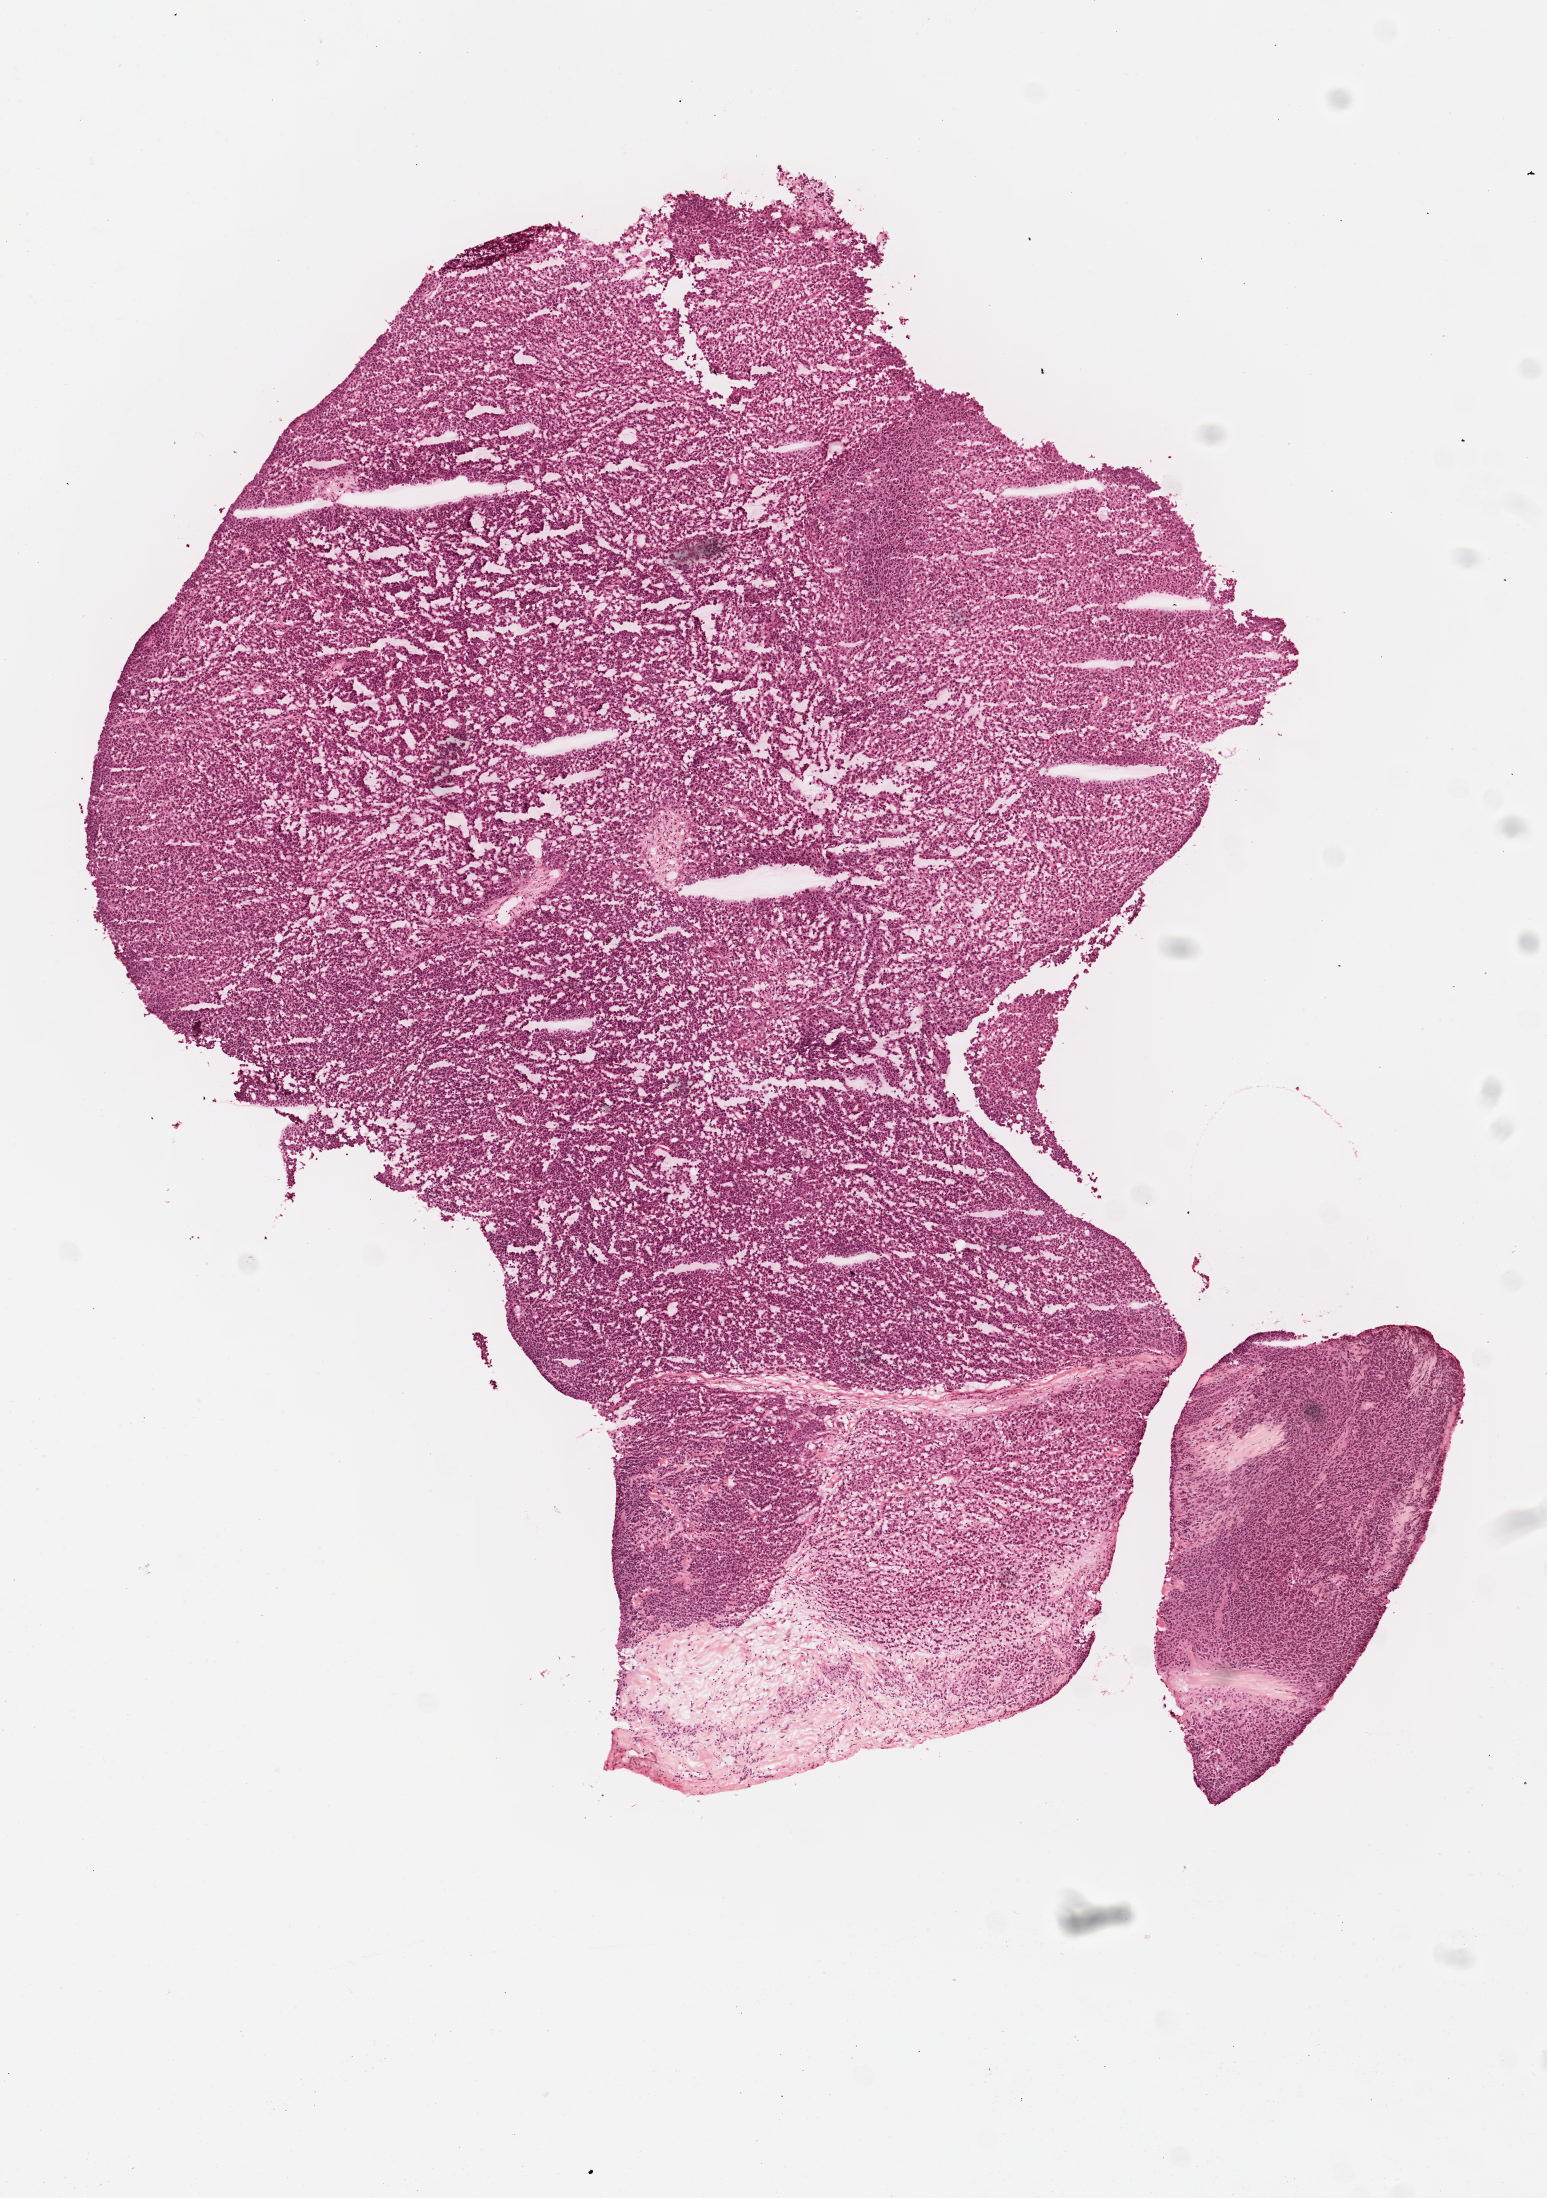
H&E whole-slide image, shown as a low-resolution overview of the whole scanned area (about 6.1 x 8.6 mm, from a 40x scan), formalin-fixed paraffin-embedded (FFPE) diagnostic section, sample: primary tumour, skin. Male, age 59 years at initial diagnosis.
Histologic diagnosis: Malignant melanoma, NOS.